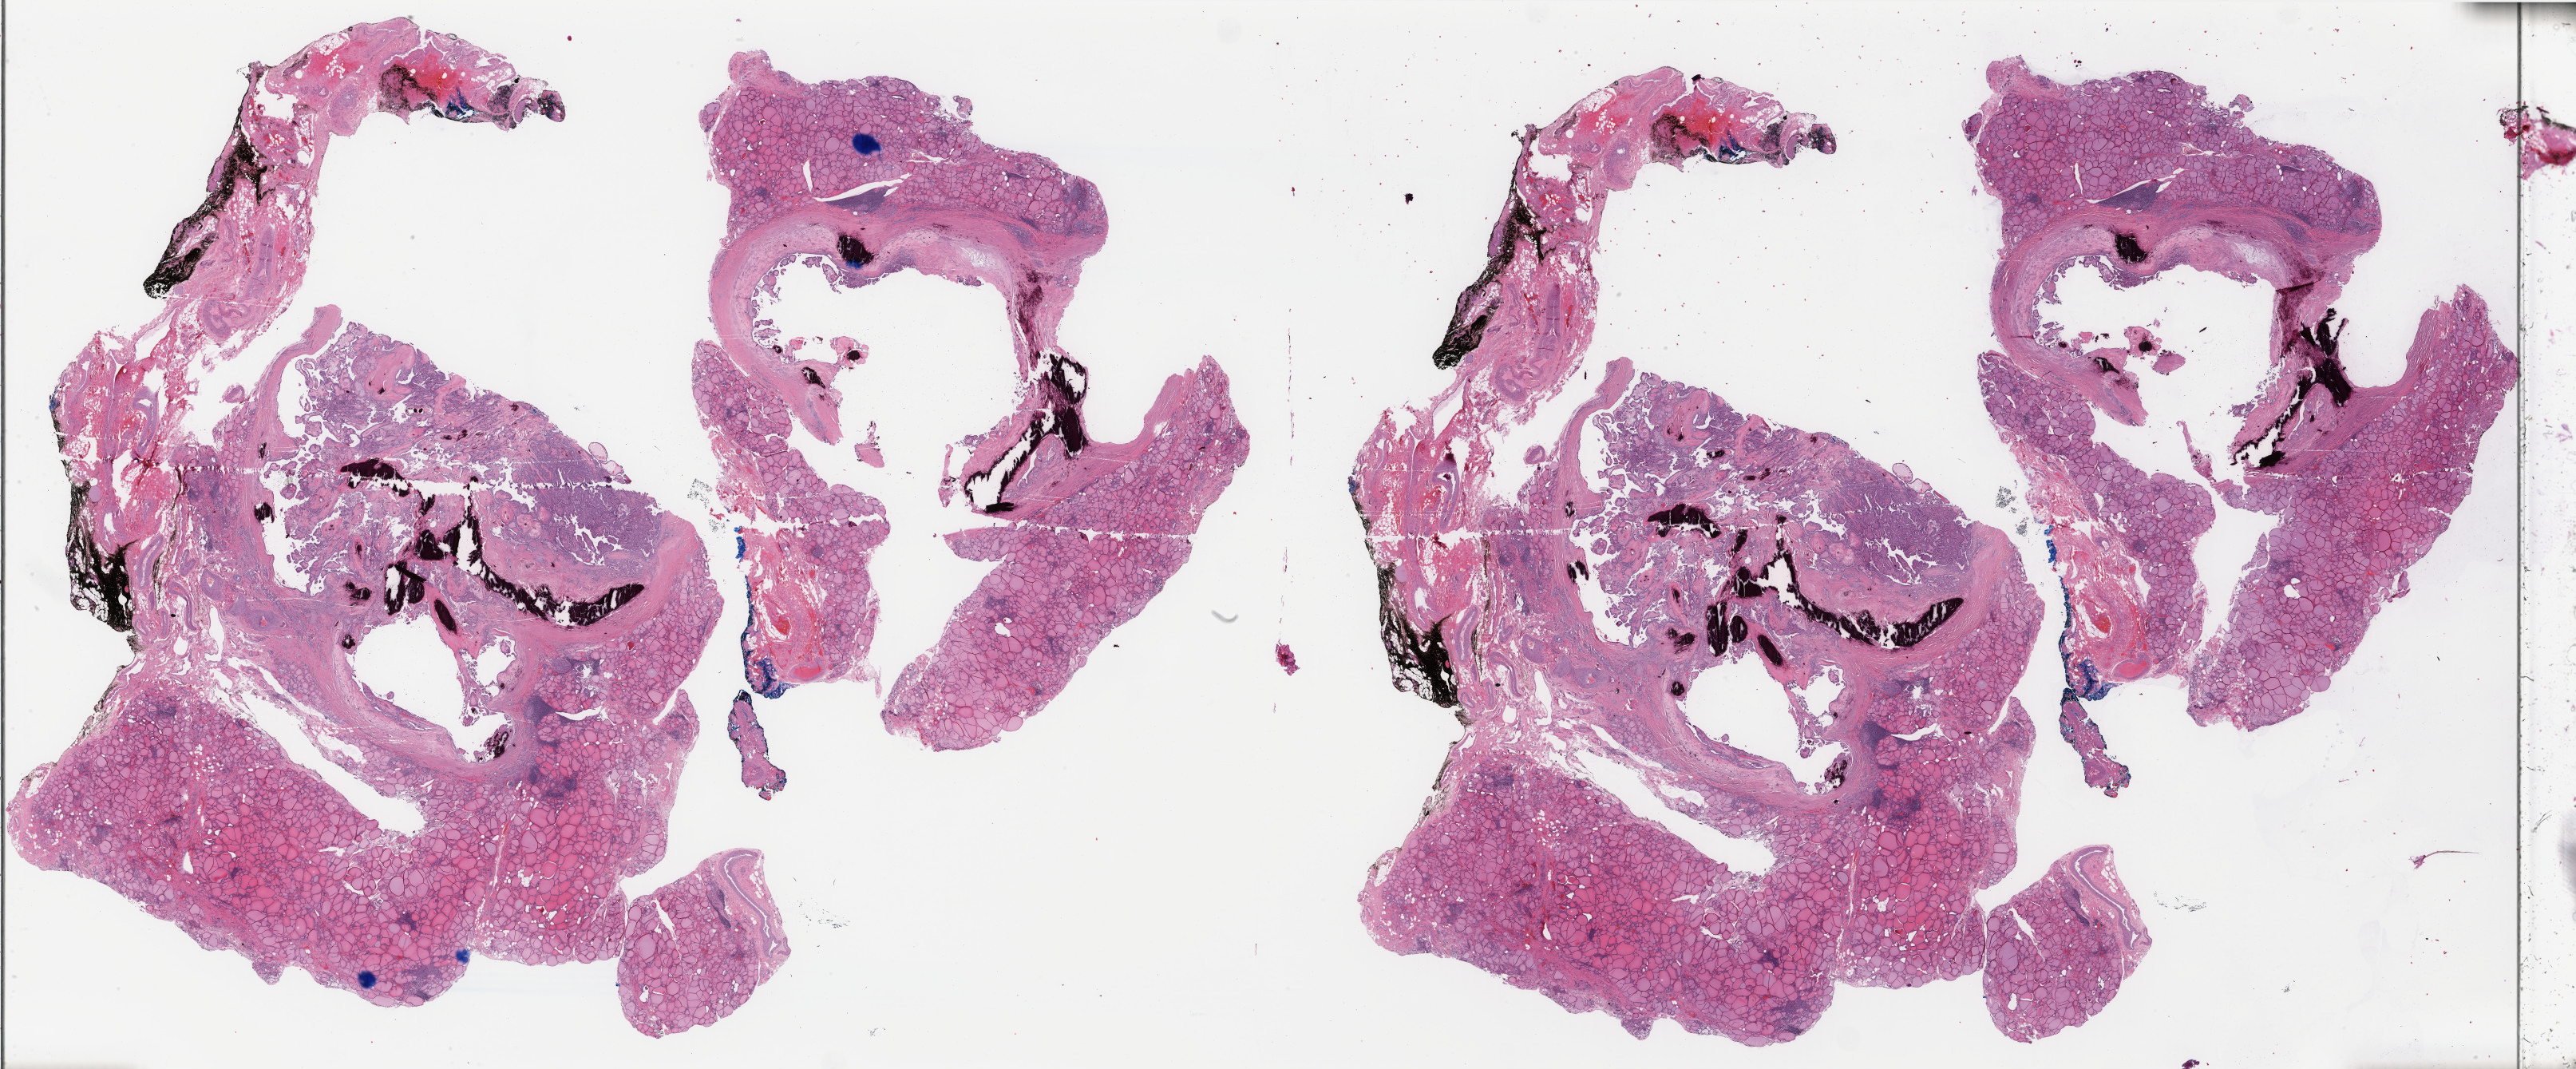
Whole-slide histology image, Hematoxylin and eosin (H&E) stained — a low-resolution overview of the entire scanned area, about 51.2 x 21.3 mm (acquisition: 40x scan); formalin-fixed paraffin-embedded (FFPE) diagnostic section; sample: primary tumour, thyroid. Male, age 56 years at initial diagnosis.
- diagnosis: Papillary adenocarcinoma, NOS (thyroid gland)
- lymph nodes positive (case pathology): 0 of 6 examined
- AJCC pathologic stage: I (7th edition)